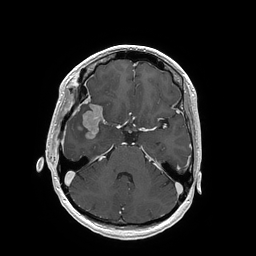
Brain MRI from a brain-tumour surgery series, one axial slice; position 113 of 202 along the scan axis; T1-weighted post-contrast; 256 × 256 image matrix, field of view 250 × 250 mm. Case-level facts recorded for this patient, not image findings: histopathology: Glioblastoma; WHO grade: 4; IDH mutation: no; tumour location: Right Insular.
Annotated regions visible in this slice (manually delineated by an expert):
- tumour: bounding box <82,105,103,139> (left, top, right, bottom; pixels)